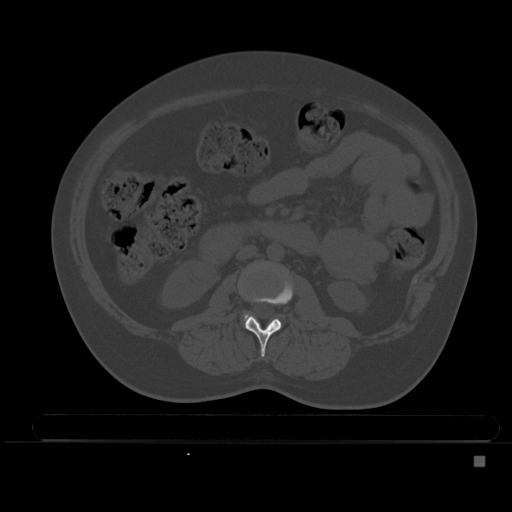
CT including the spine, one axial slice; position 165 of 495 along the scan axis; bone window (W 1800 / L 400 HU); 512 × 512 image matrix, field of view 404 × 404 mm. Patient: female, 33 years. Case-level facts recorded for this patient, not image findings: primary cancer: breast.
Structures marked on this image (semi-automatically segmented with operator editing):
- L2 vertebra: bounding box <245,278,294,357> (left, top, right, bottom; pixels)
- L3 vertebra: <244,314,250,322>